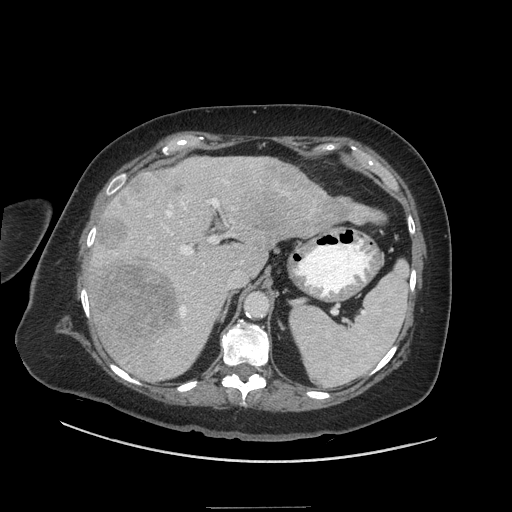
Contrast-enhanced abdominal CT (liver protocol), one axial slice; position 34 of 81 along the scan axis; soft-tissue window (W 400 / L 40 HU); 2.5 mm slice thickness; 512 × 512 image matrix, field of view 440 × 440 mm. From the clinical record (not read from this slice): diagnosis: hepatocellular carcinoma (patient treated with transarterial chemoembolisation; whether this scan precedes or follows treatment is not stated here); TNM stage (as recorded): Stage-II; Child-Pugh class: A; tumour differentiation: moderately differentiated; tumour size: 1.7 cm.
Structures marked on this image (semi-automatically segmented with operator editing):
- liver parenchyma outside the tumour (the mass and vessels are separate outlines, so this box may not span the whole liver): bounding box [x1, y1, x2, y2] px = [90, 156, 371, 380]
- mass: [87, 164, 389, 341]
- liver vessels: [100, 160, 254, 329]